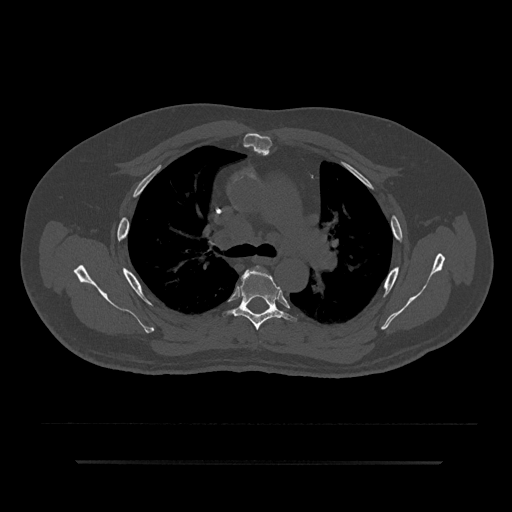
CT including the spine, one axial slice; slice 577 of 797 in the series (ordered by position); reconstruction kernel Br40s/3; 120 kVp; bone window (W 1800 / L 400 HU); 0.5 mm slice thickness; 512 × 512 image matrix, field of view 464 × 464 mm. Patient: male, 59 years. Case-level facts recorded for this patient, not image findings: primary cancer: bile ducts.
Outlined on this slice (semi-automatically segmented with operator editing):
- T4 vertebra: bounding box <252,266,263,272> (left, top, right, bottom; pixels)
- T5 vertebra: <226,269,292,331>